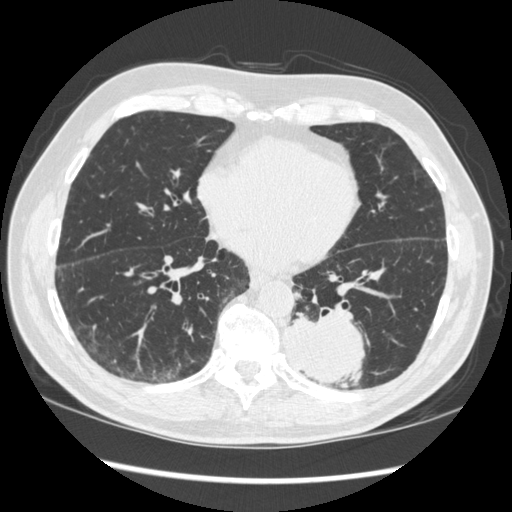
Low-dose screening chest CT, one axial slice. Position 126 of 348 along the scan axis. Reconstruction kernel STANDARD. 120 kVp. Lung window (W 1500 / L -600 HU). 1.25 mm slice thickness. 512 × 512 image matrix, field of view 360 × 360 mm.
Structures marked on this image (manually delineated by an expert):
- lesion 1 (tumor, lower lobe of left lung): bounding box [x1, y1, x2, y2] px = [285, 312, 366, 389]